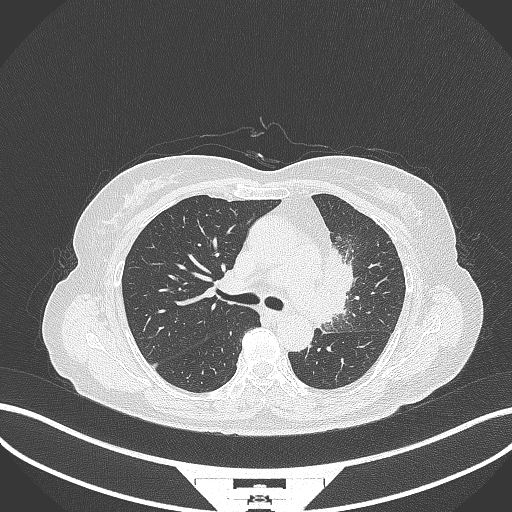
Chest CT, one axial slice. Position 212 of 382 along the scan axis. 120 kVp. Lung window (W 1500 / L -600 HU). 512 × 512 image matrix, field of view 400 × 400 mm. Patient: female, 64 years. Case-level facts recorded for this patient, not image findings: clinical TNM (as recorded): T2a N2 M0.
Structures marked on this image (rectangle marked by the reading radiologist):
- lung tumour (recorded histology: adenocarcinoma): bounding box <321,236,362,325> (left, top, right, bottom; pixels)